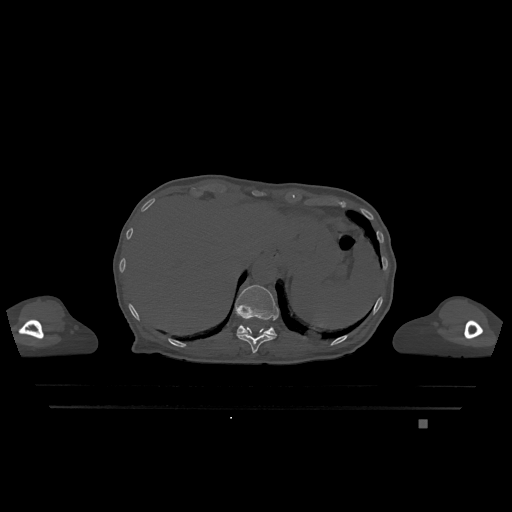
CT including the spine, one axial slice; position 564 of 1317 along the scan axis; bone window (W 1800 / L 400 HU); 0.5 mm slice thickness; 512 × 512 image matrix, field of view 500 × 500 mm. Patient: female, 74 years. From the clinical record (not read from this slice): primary cancer: lung.
Structures marked on this image (semi-automatically segmented with operator editing):
- T11 vertebra: bounding box [x1, y1, x2, y2] px = [237, 327, 276, 353]
- T12 vertebra: [235, 285, 279, 336]